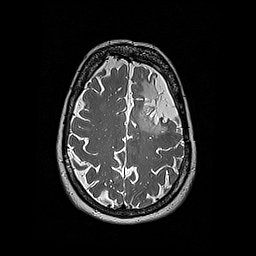
Brain MRI from a brain-tumour surgery series, one axial slice; position 134 of 192 along the scan axis; 1 mm slice thickness; 256 × 256 image matrix. From the clinical record (not read from this slice): histopathology: Oligodendroglioma; WHO grade: 2; IDH mutation: yes.
Outlined on this slice (expert manual segmentation):
- tumour: bounding box (x1, y1, x2, y2) in pixels: (135, 81, 158, 133)